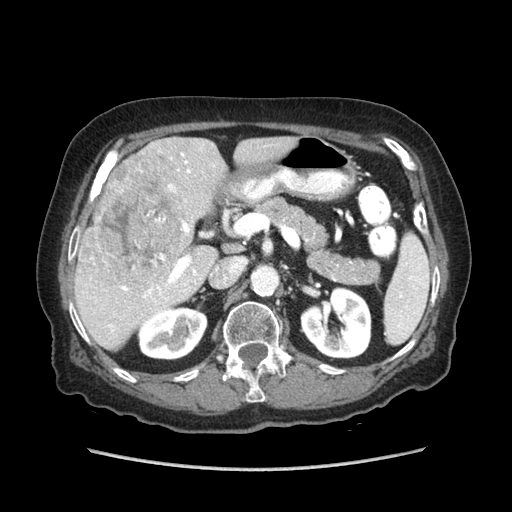
Contrast-enhanced abdominal CT (liver protocol), one axial slice; slice 40 of 89 in the series (ordered by position); reconstruction kernel STANDARD; 140 kVp; soft-tissue window (W 400 / L 40 HU); 512 × 512 image matrix, field of view 360 × 360 mm. From the clinical record (not read from this slice): diagnosis: hepatocellular carcinoma (patient treated with transarterial chemoembolisation; whether this scan precedes or follows treatment is not stated here); TNM stage (as recorded): Stage-IIIA; Child-Pugh class: A; tumour differentiation: well differentiated; tumour size: 11 cm.
Annotated regions visible in this slice (semi-automatically segmented with operator editing):
- liver parenchyma outside the tumour (the mass and vessels are separate outlines, so this box may not span the whole liver): bounding box [x1, y1, x2, y2] px = [74, 136, 296, 350]
- mass: [92, 144, 184, 282]
- liver vessels: [108, 153, 197, 332]